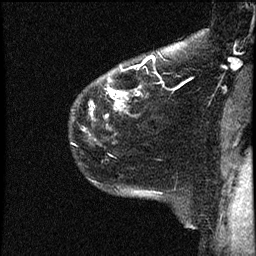
Breast MRI (dynamic contrast-enhanced), one sagittal slice. Slice 38 of 44 in the series (ordered by position). Dynamic contrast-enhanced study with each time point stored as its own series, time point 2 of 4 at this slice position (early post-contrast, ordered by acquisition time). 1.5 T. TE 4.2 ms, TR 17.7 ms. 256 × 256 image matrix. Female patient, age 52 years. Case-level facts recorded for this patient, not image findings: setting: breast cancer imaged before/during neoadjuvant chemotherapy; receptor status: HR-positive, HER2-negative.
Annotated regions visible in this slice (semi-automatic segmentation, software-assisted and operator-edited):
- analysis volume of interest (the breast-tissue region the enhancement analysis was run in; not a lesion): bounding box <69,49,163,147> (left, top, right, bottom; pixels)
- tumour enhancement mask (voxels above the 100 % enhancement threshold inside the analysis volume of interest): <90,55,155,115>